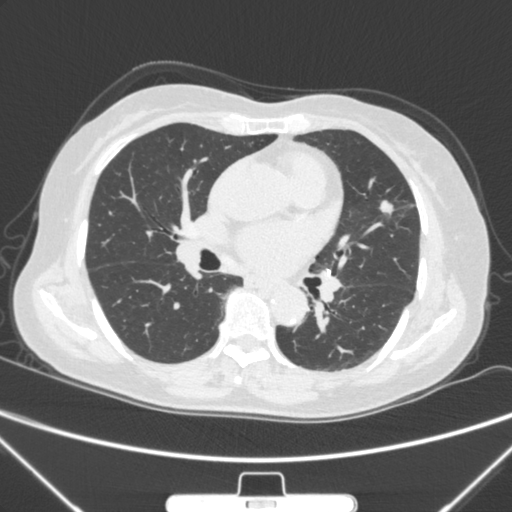
Chest CT, one axial slice. Position 147 of 300 along the scan axis. Lung window (W 1500 / L -600 HU). 1 mm slice thickness. 512 × 512 image matrix, field of view 350 × 350 mm. Female patient, age 70 years. From the clinical record (not read from this slice): clinical TNM (as recorded): T1b N0 M0.
Structures marked on this image (rectangle marked by the reading radiologist):
- lung tumour (recorded histology: adenocarcinoma): bounding box [x1, y1, x2, y2] px = [372, 192, 401, 220]